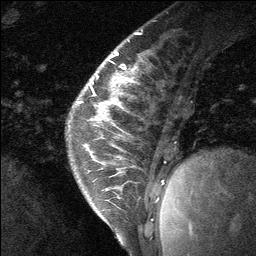
Breast MRI (dynamic contrast-enhanced), one sagittal slice; position 22 of 64 along the scan axis; dynamic contrast-enhanced study with each time point stored as its own series, time point 2 of 3 at this slice position (early post-contrast, ordered by acquisition time); 1.5 T; TE 4.8 ms, TR 27 ms; 2 mm slice thickness; 256 × 256 image matrix. Patient: female, 26 years. Case-level facts recorded for this patient, not image findings: setting: breast cancer imaged before/during neoadjuvant chemotherapy; receptor status: HR-positive, HER2-negative.
Outlined on this slice (semi-automatically segmented with operator editing):
- analysis volume of interest (the breast-tissue region the enhancement analysis was run in; not a lesion): bounding box [x1, y1, x2, y2] px = [86, 43, 135, 138]
- tumour enhancement mask (voxels above the 90 % enhancement threshold inside the analysis volume of interest): [115, 52, 117, 54]